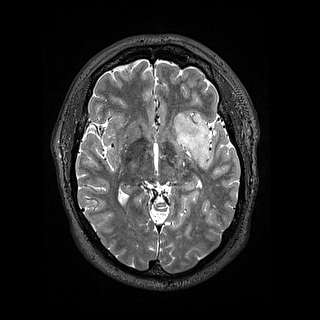
Brain MRI from a brain-tumour surgery series, one axial slice; position 89 of 144 along the scan axis; 1.2 mm slice thickness; 320 × 320 image matrix. Case-level facts recorded for this patient, not image findings: histopathology: Astrocytoma; WHO grade: 2; IDH mutation: yes.
Outlined on this slice (manually delineated by an expert):
- tumour: bounding box (x1, y1, x2, y2) in pixels: (173, 108, 211, 166)